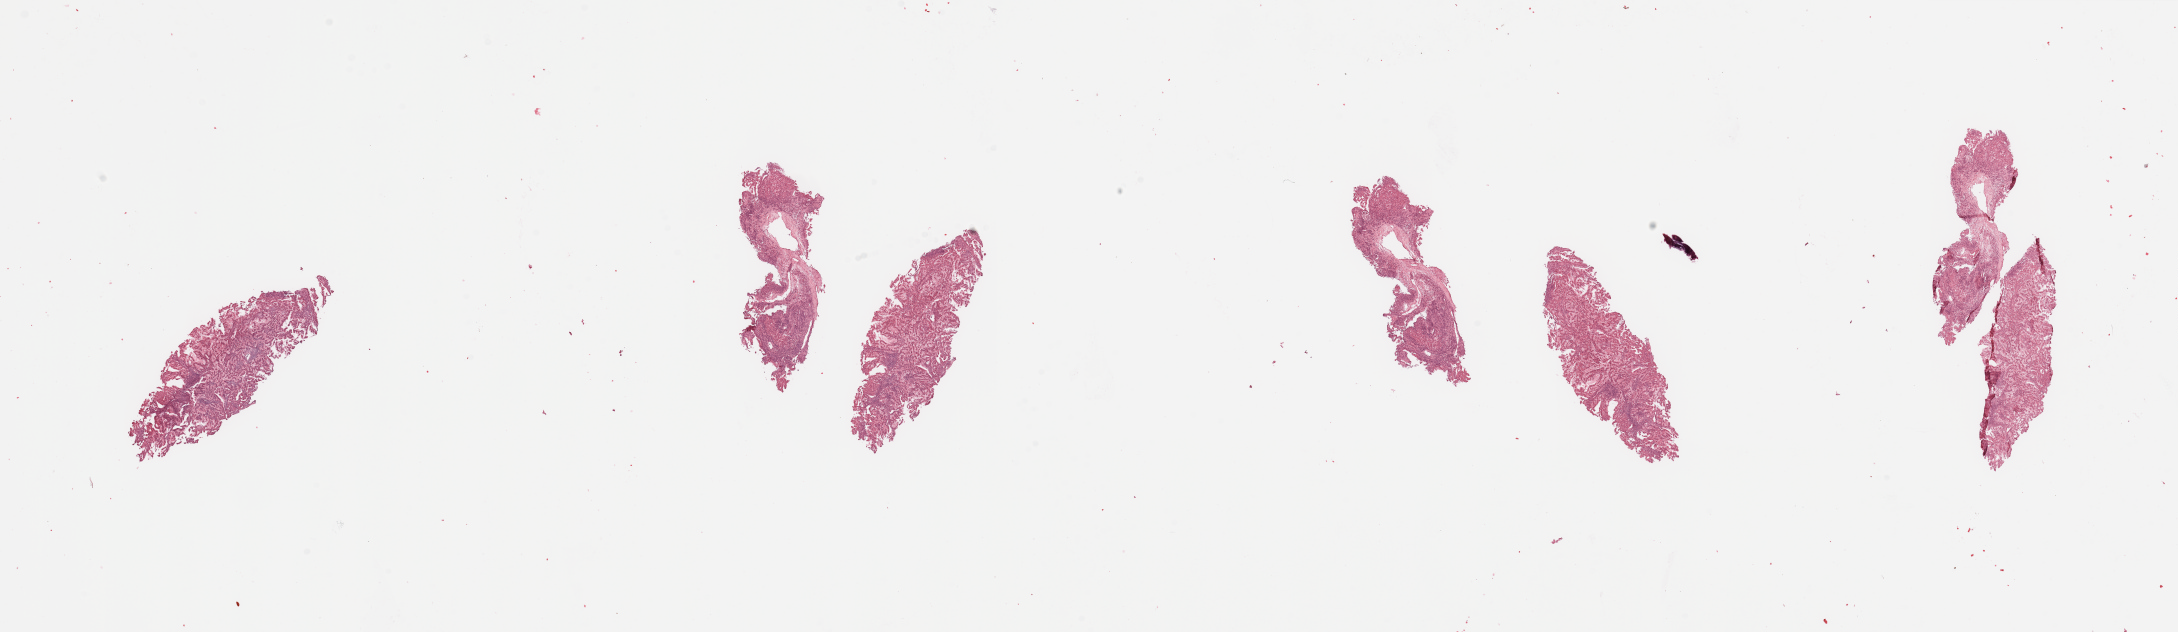
Whole-slide histology image, Hematoxylin and eosin (H&E) stained — a low-resolution overview of the entire scanned area, about 34.5 x 10.0 mm (slide scanned at 20x); tumour tissue sample, sampled site: kidney. Male, 64 y/o. Histologic grade: G2 (moderately differentiated). Pathologist review of this section (percent, as recorded): tumour nuclei 85%, necrosis 5%.
AJCC pathologic stage: I. Primary tumour site (as recorded): upper pole. Histologic diagnosis: Renal cell carcinoma, NOS.